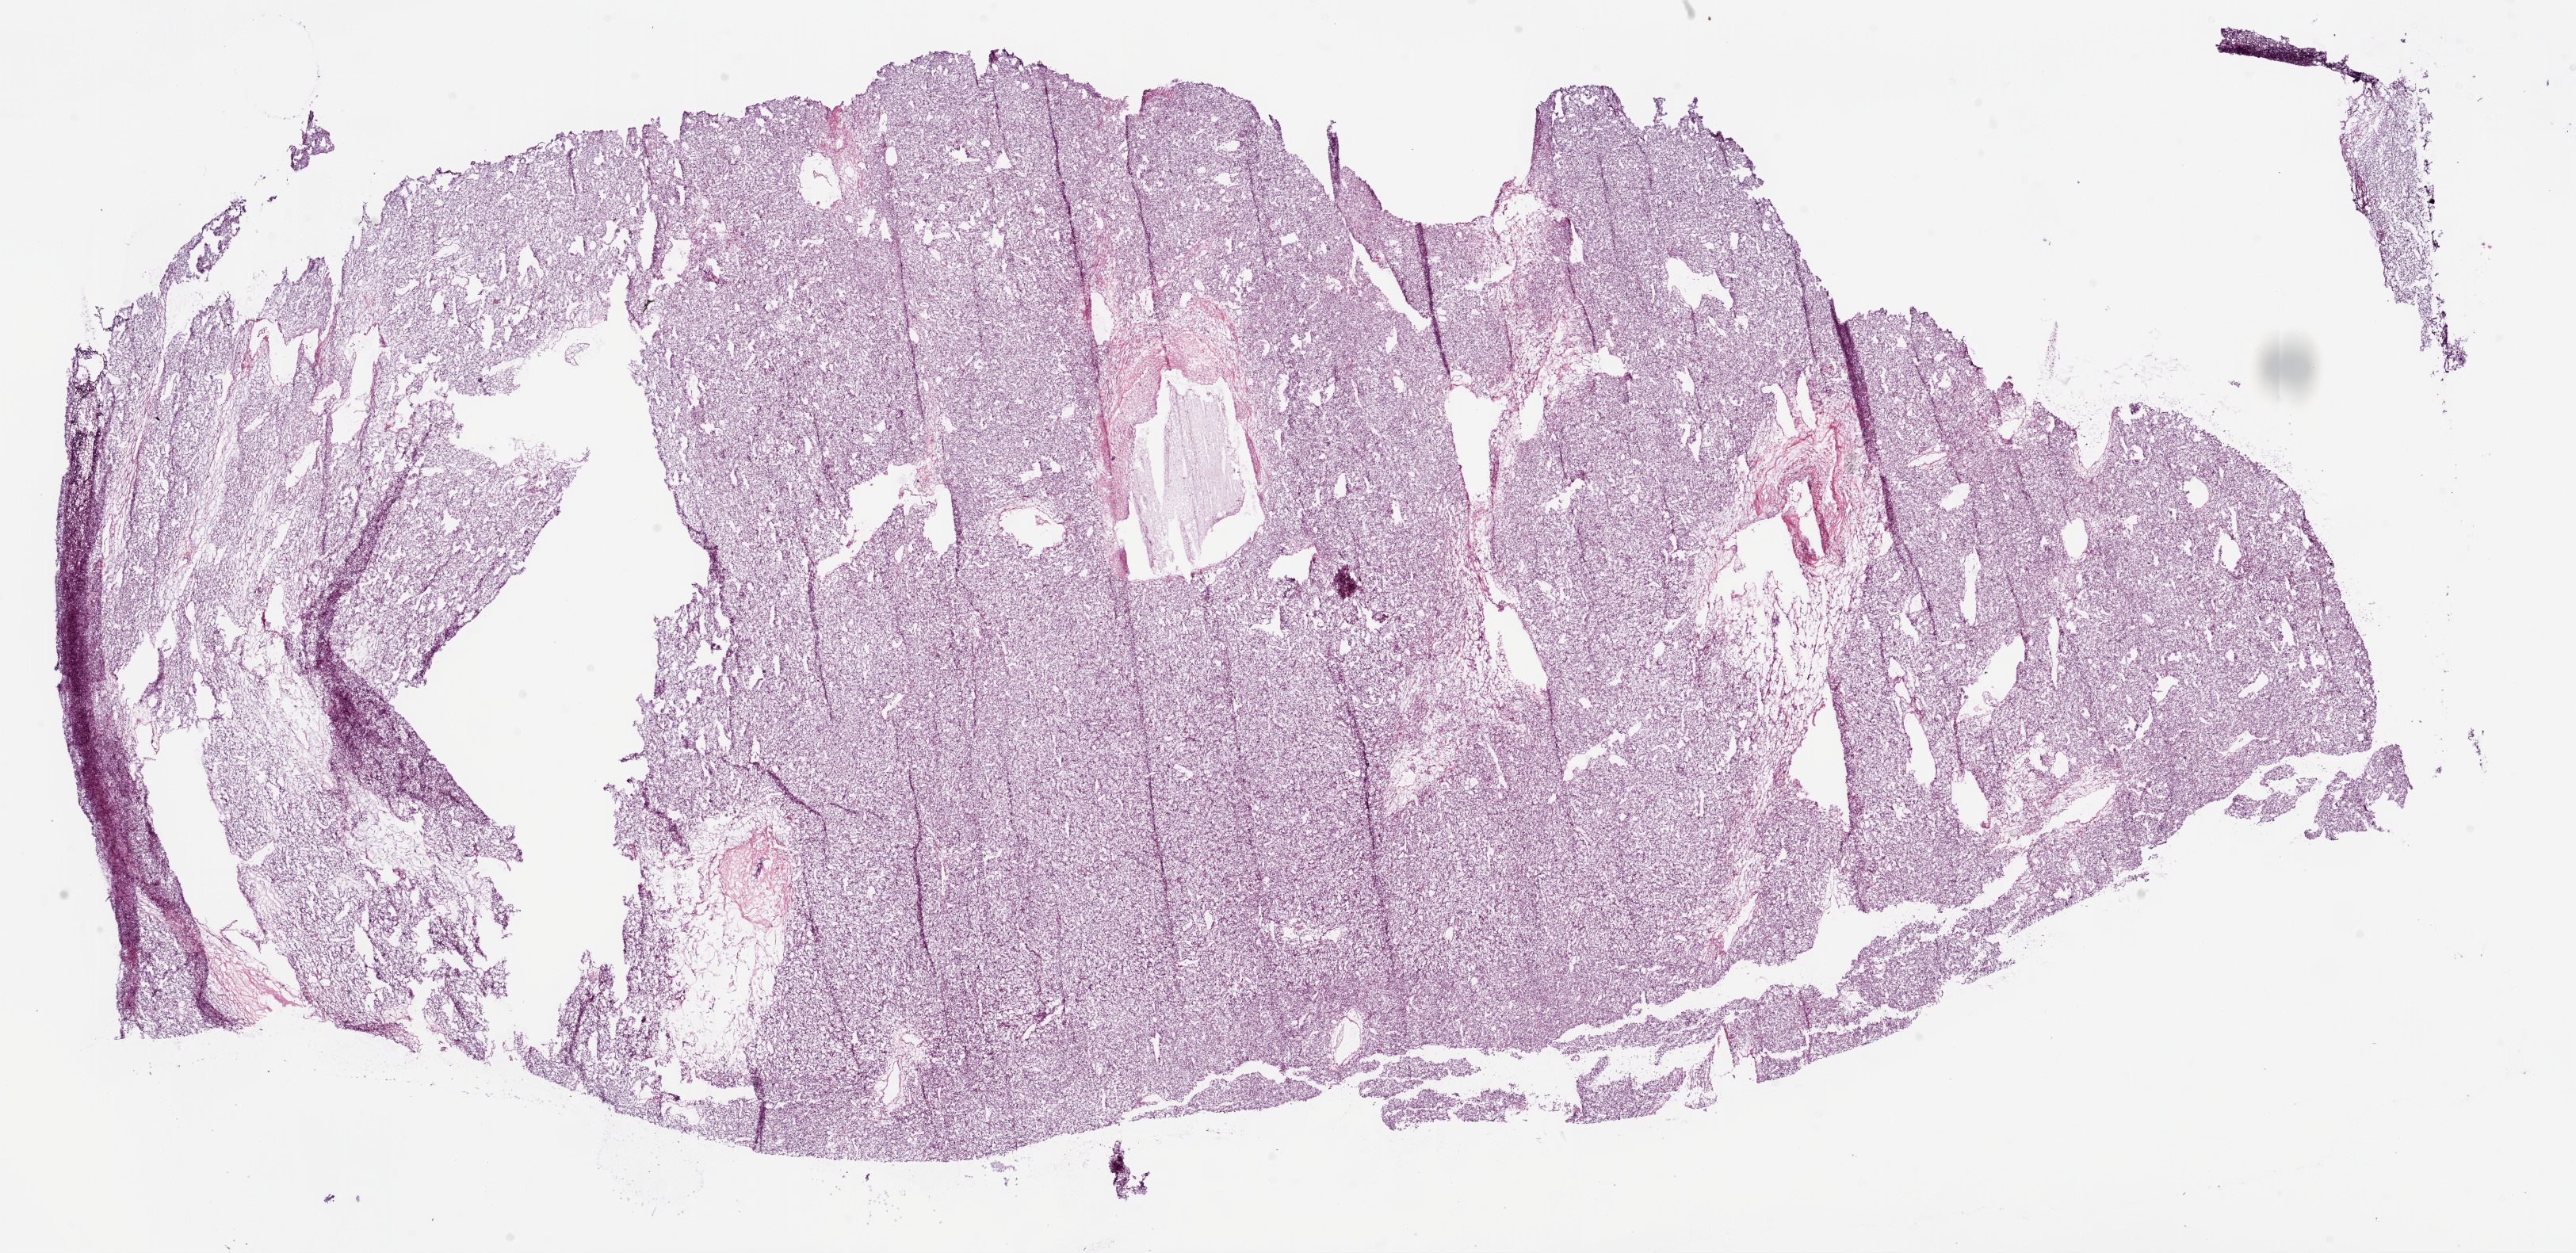
H&E whole-slide image — a low-resolution overview of the entire scanned area, about 26.1 x 12.7 mm, frozen section, kidney, primary tumour sample. Patient: male, age at initial diagnosis 49 years. Histologic grade: G3 (poorly differentiated). Slide review estimates, as recorded: tumour cells 90%, tumour nuclei 90%, normal cells 0%, stromal cells 10%, necrosis 0%.
Laterality: left. Histologic diagnosis: Clear cell adenocarcinoma, NOS. AJCC pathologic stage: II.